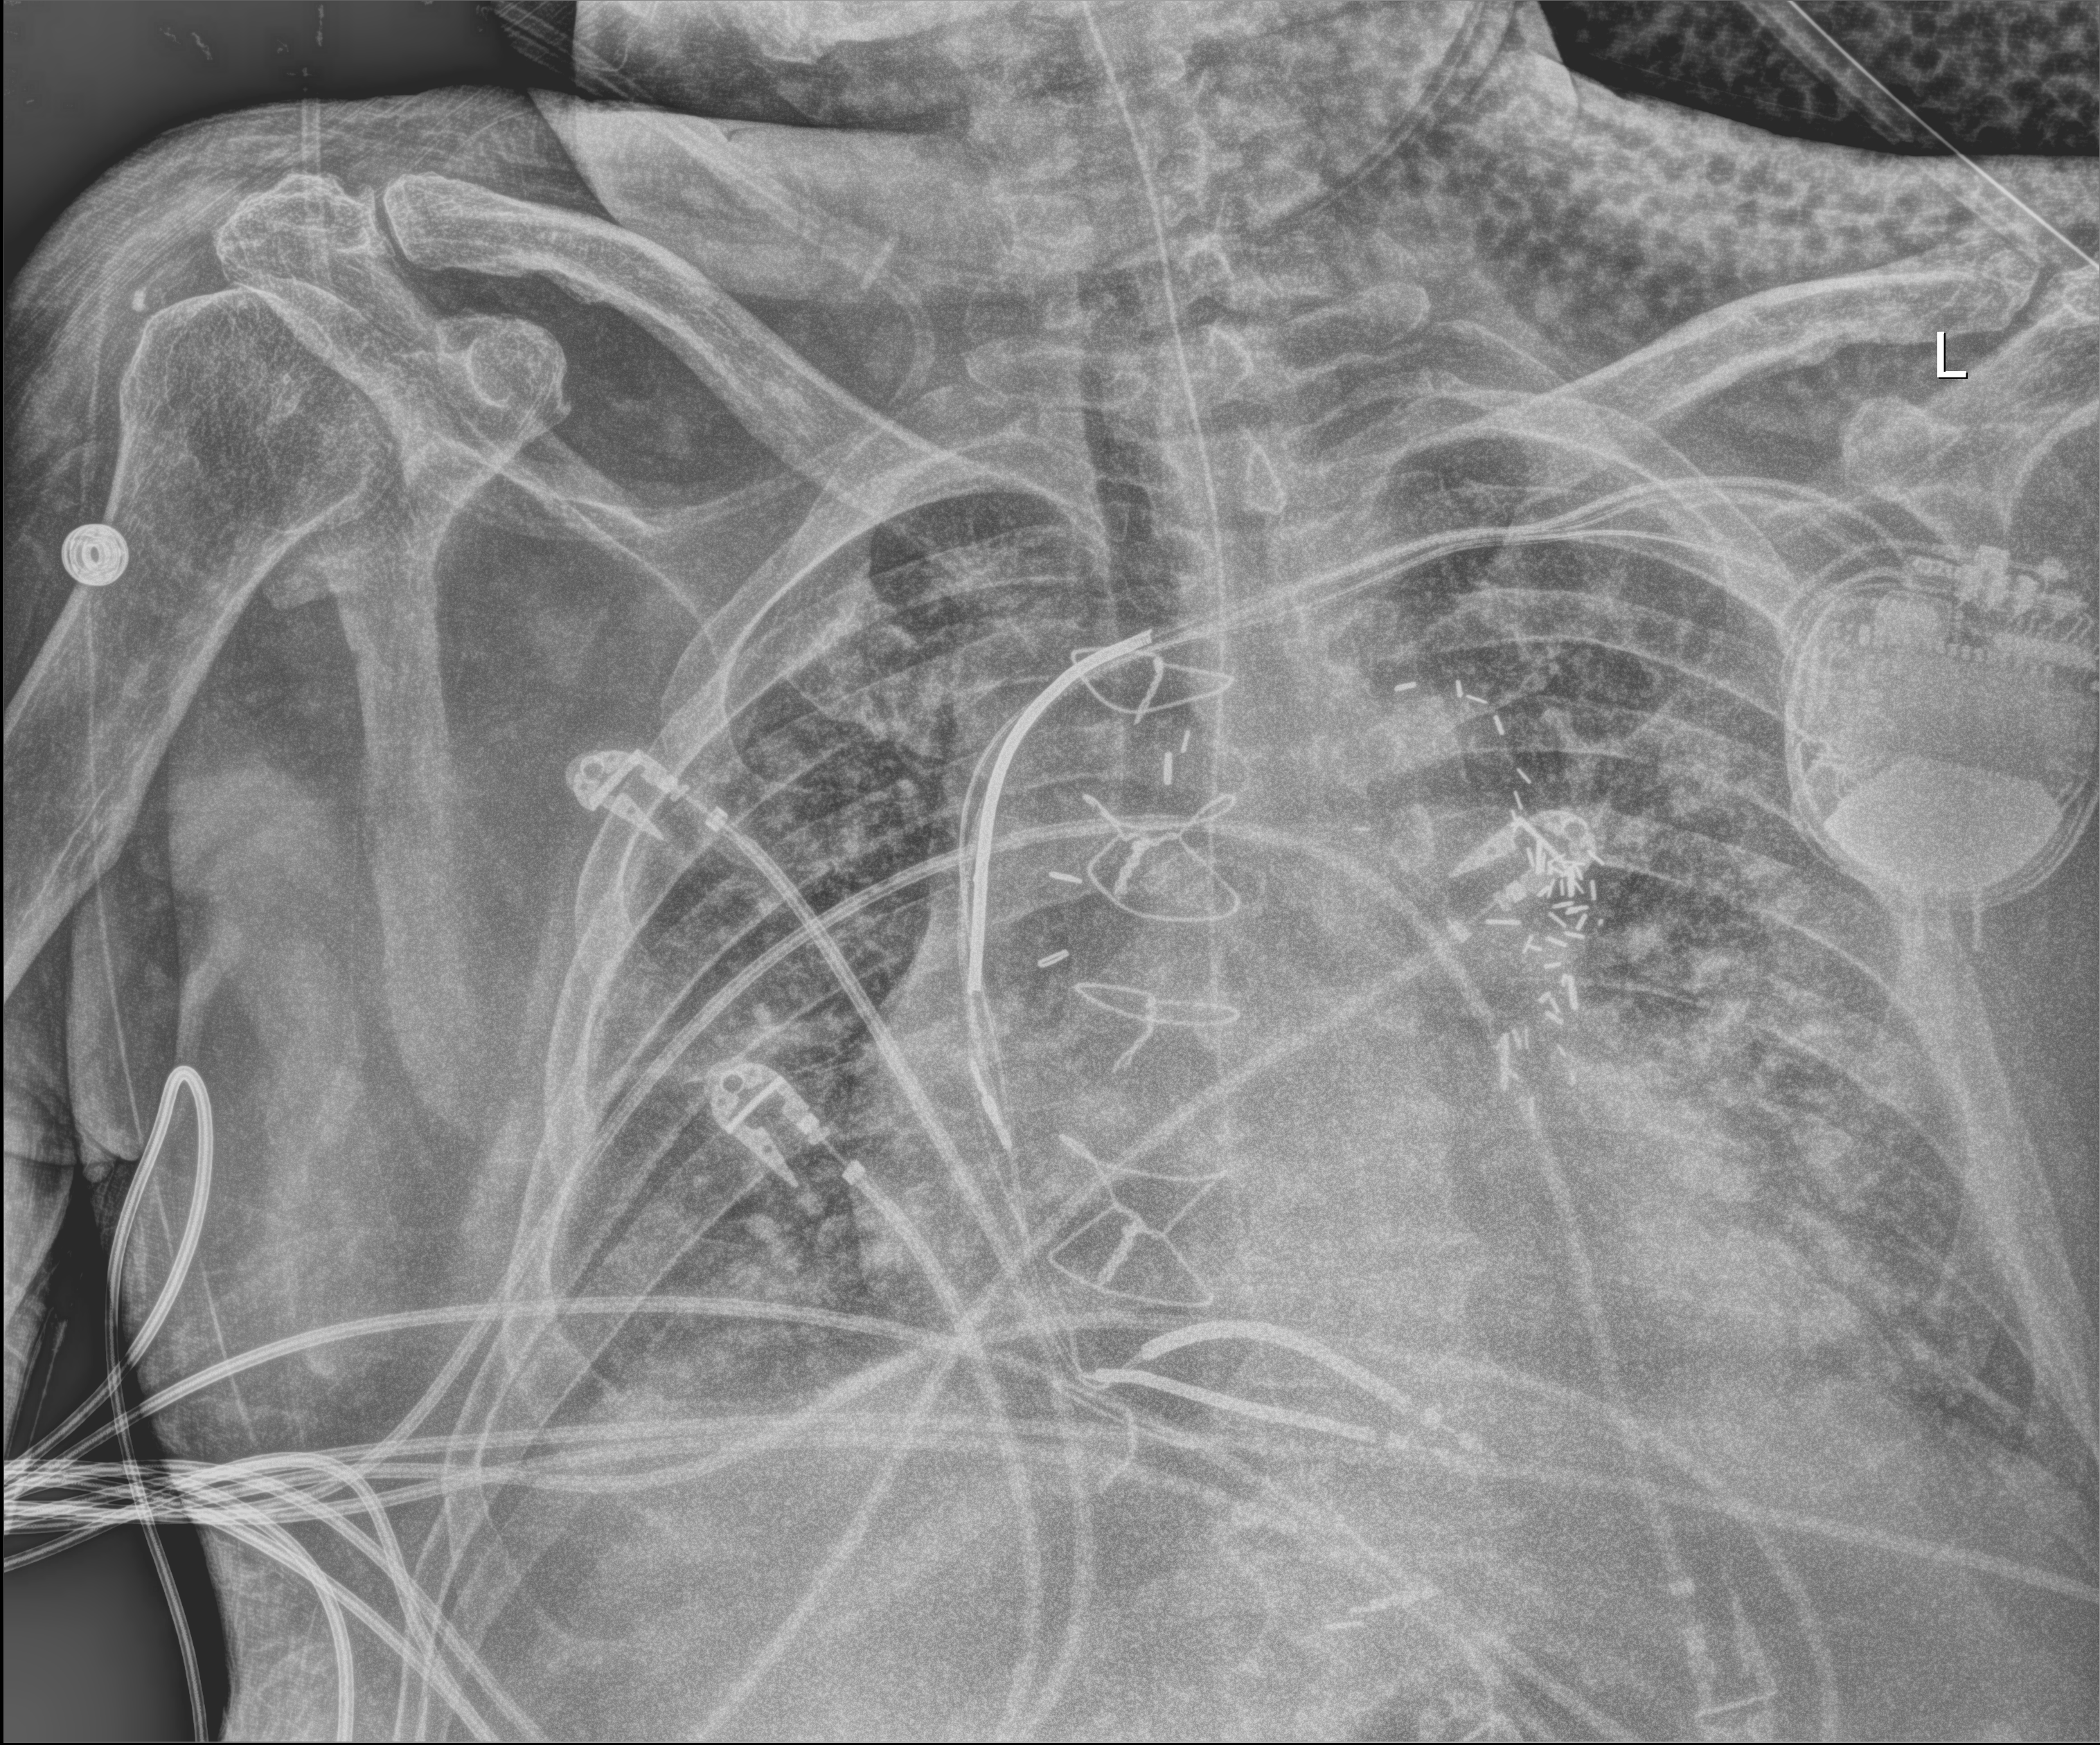
Portable chest radiograph, anteroposterior (AP) projection. Patient hospitalised with COVID-19; male, aged 60–74 years.
From the hospital-stay record, not from the radiograph (when in the stay this image was taken is not recorded): admitted to intensive care during this hospital stay: yes; mechanically ventilated during this hospital stay: yes.